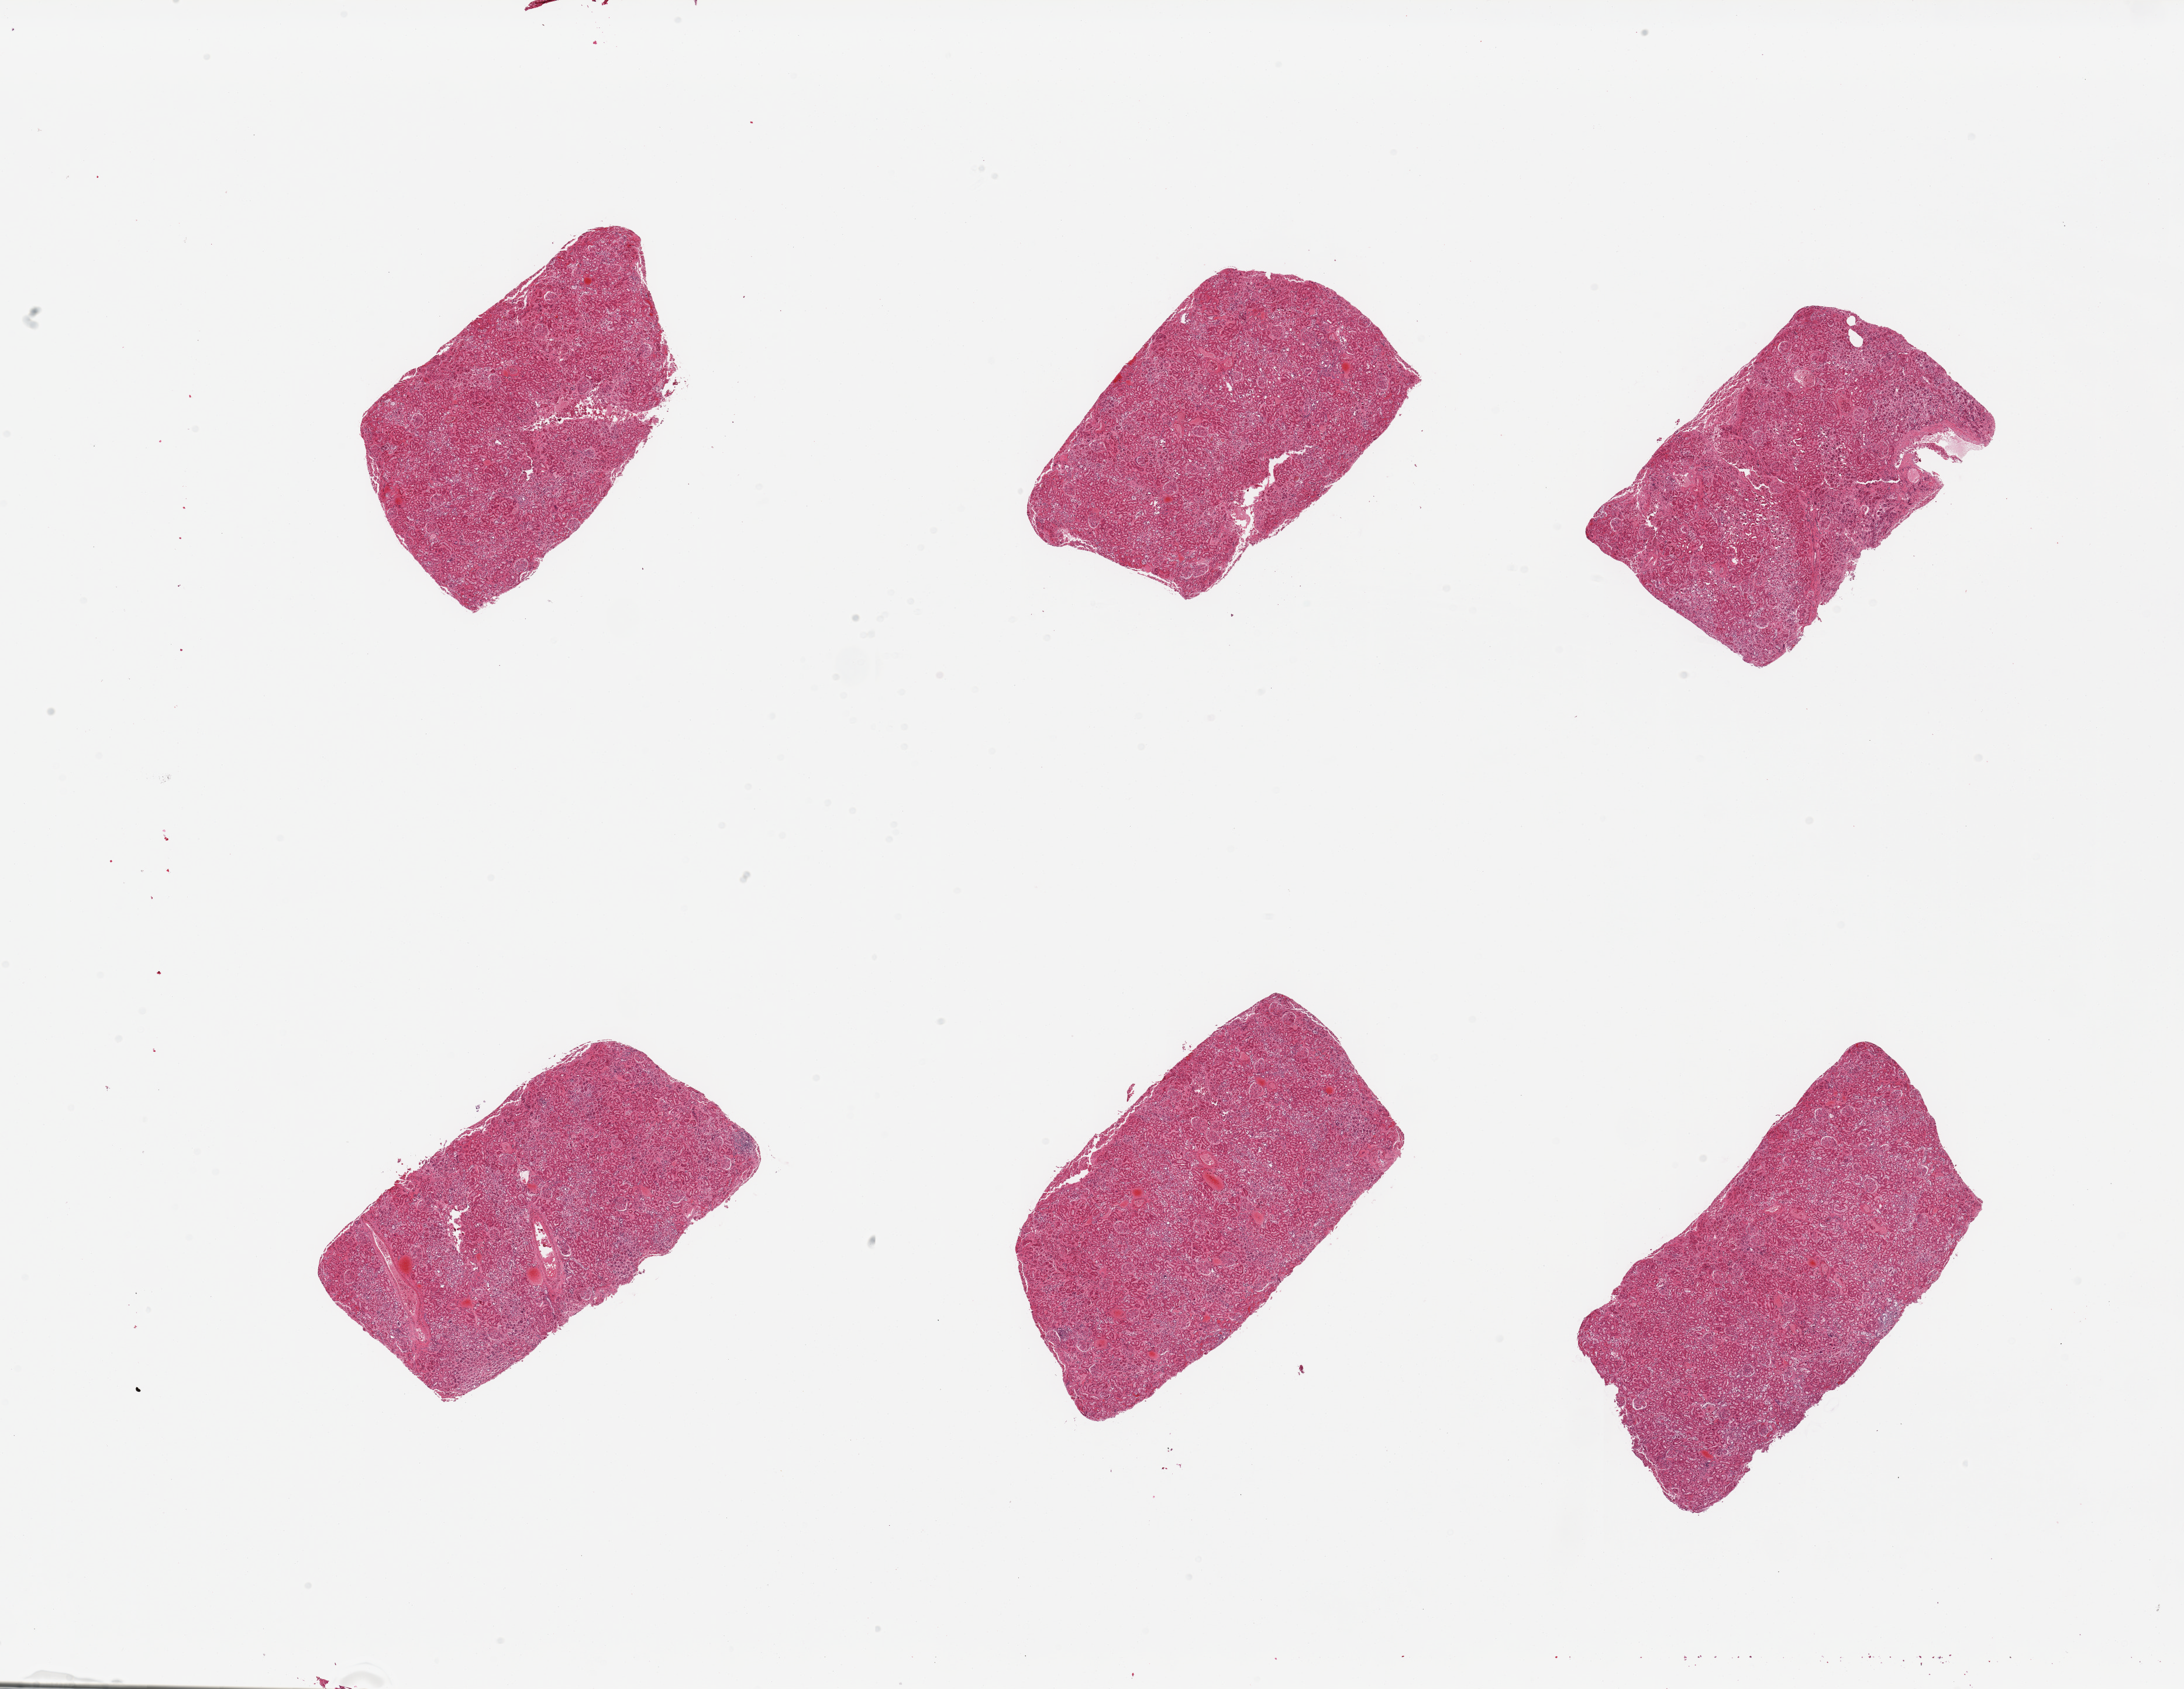
H&E whole-slide image, low-resolution overview of the scanned area, about 29.5 x 22.8 mm. PAXgene-fixed, paraffin-embedded tissue. Section of renal cortex (target tissue). Donor tissue sample.
Reviewer comment on this tissue sample: 6 pieces; congestion.